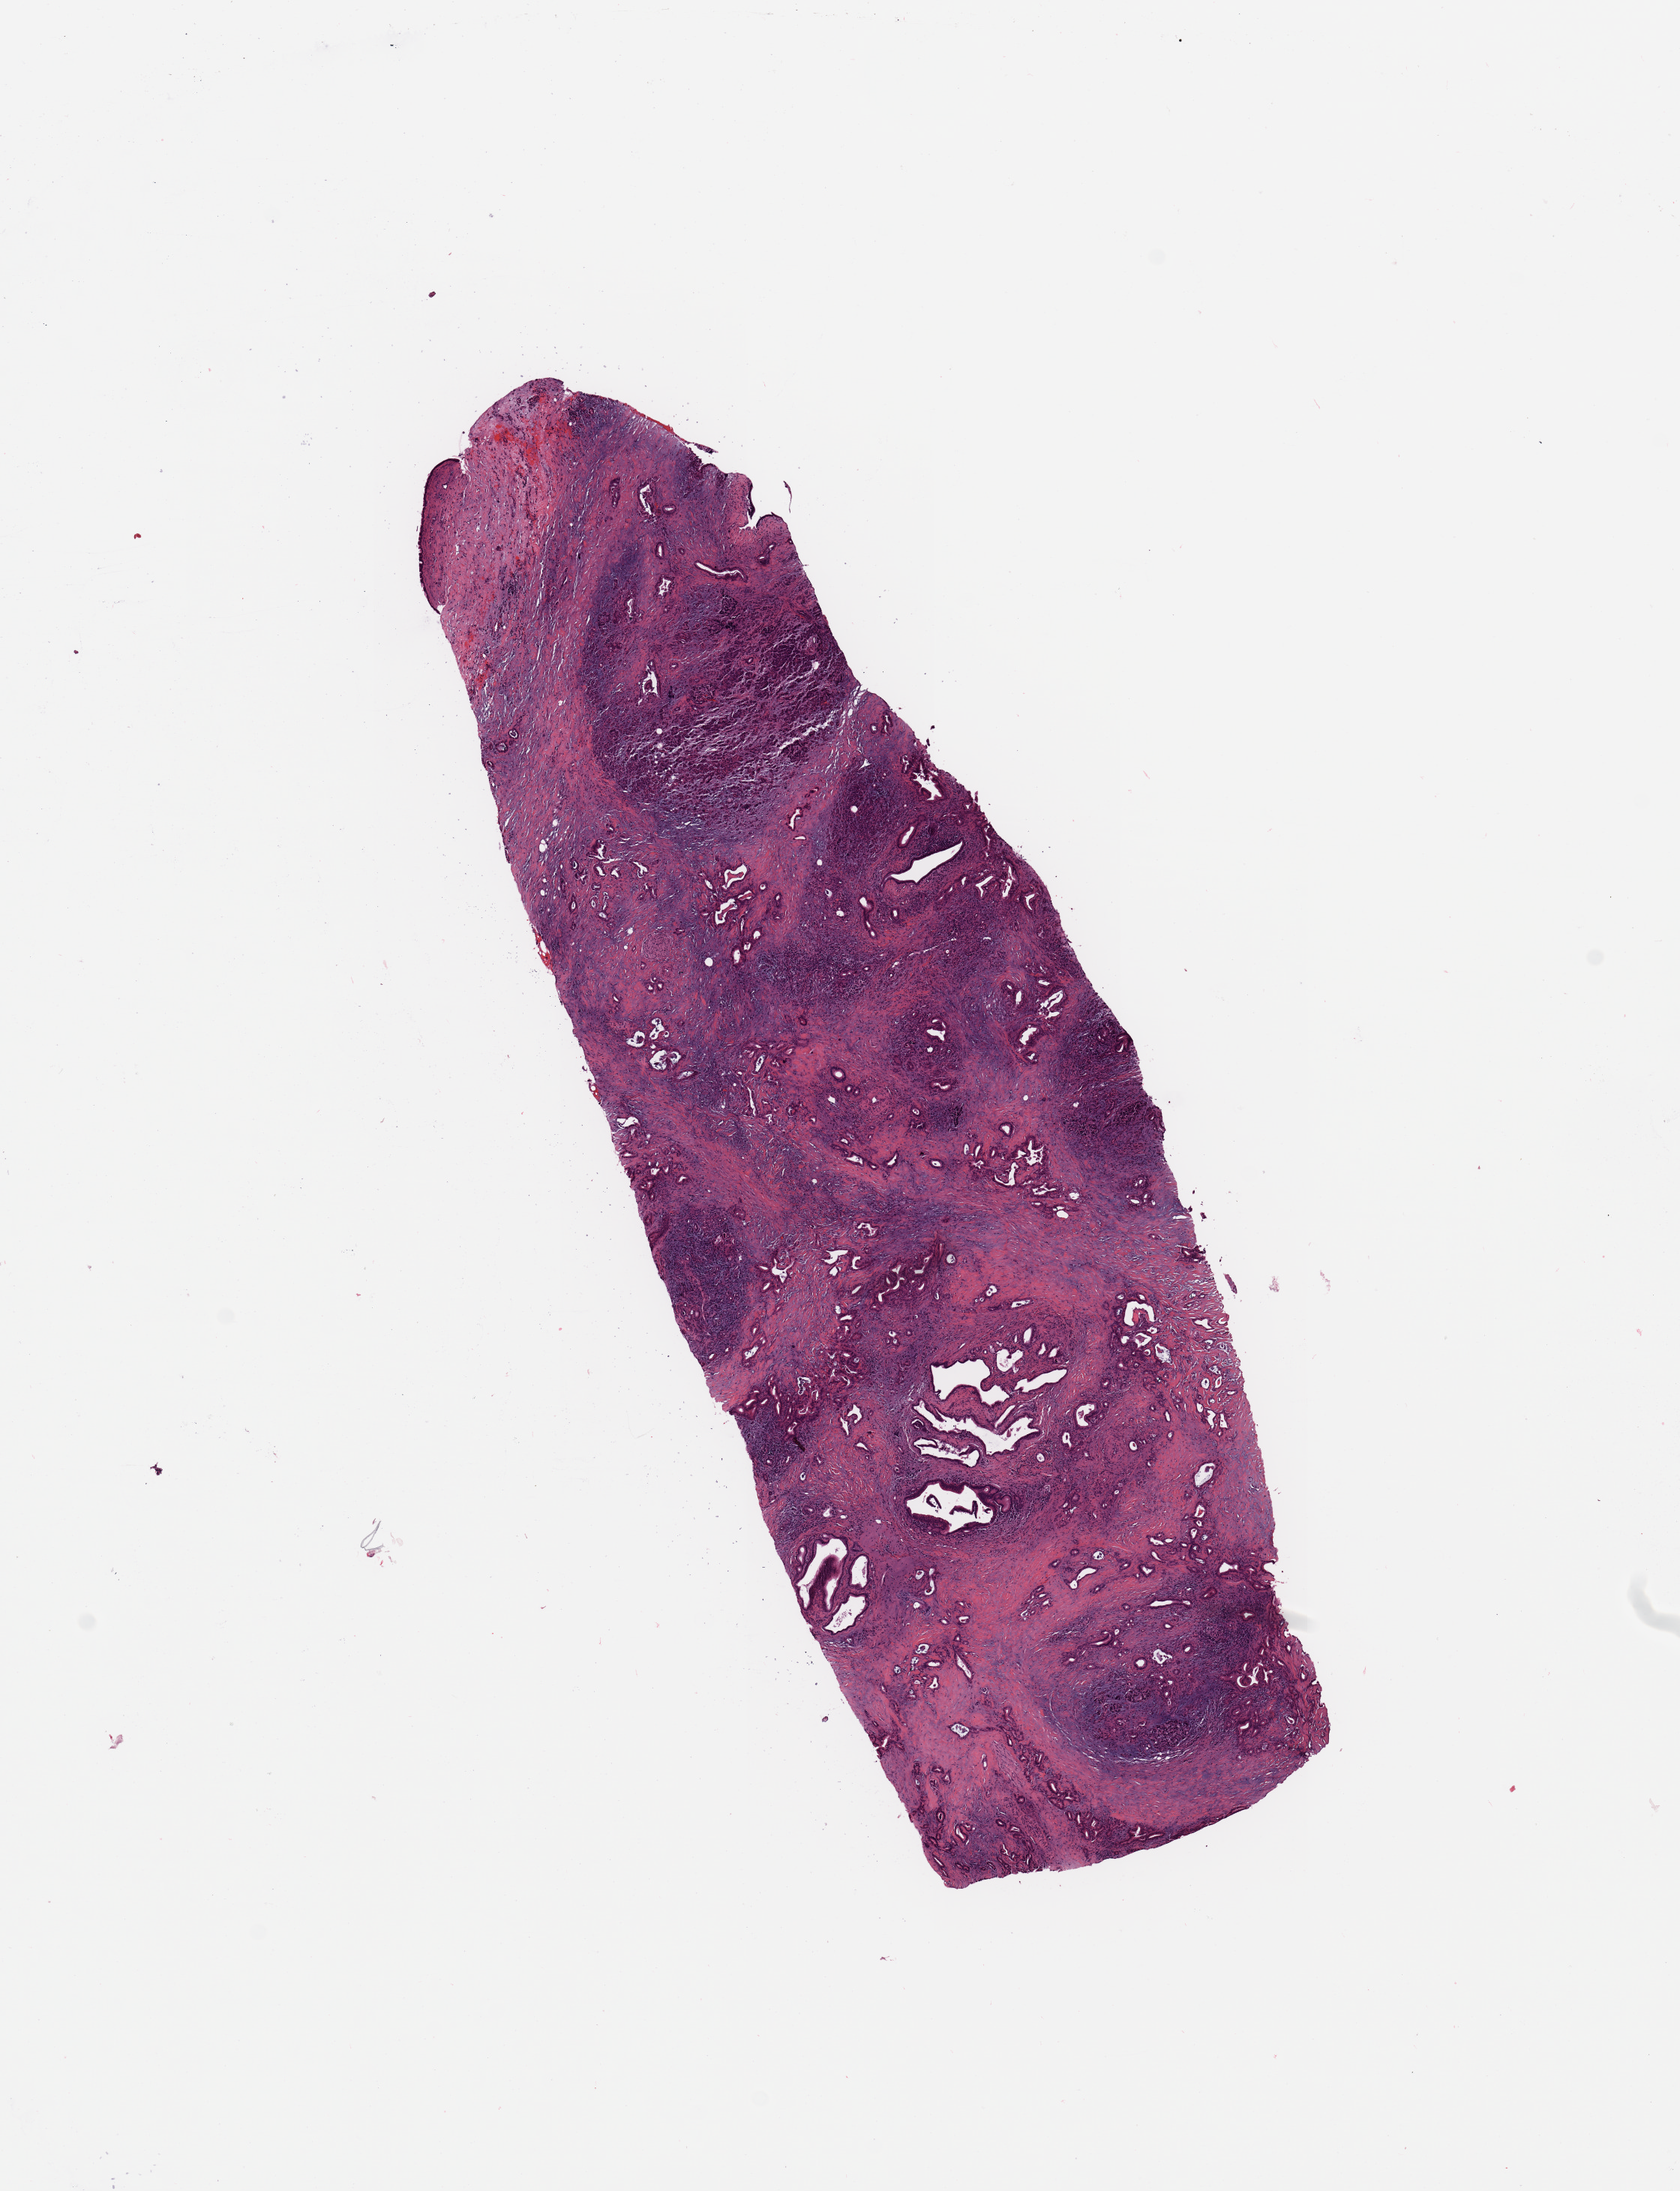
Whole-slide histology image, H&E — whole scanned area (about 8.9 x 11.6 mm, from a 20x scan) shown as a low-resolution overview. Pancreas, tissue type not recorded.
* patient diagnosis (cohort enrolment): ductal adenocarcinoma (pancreas)